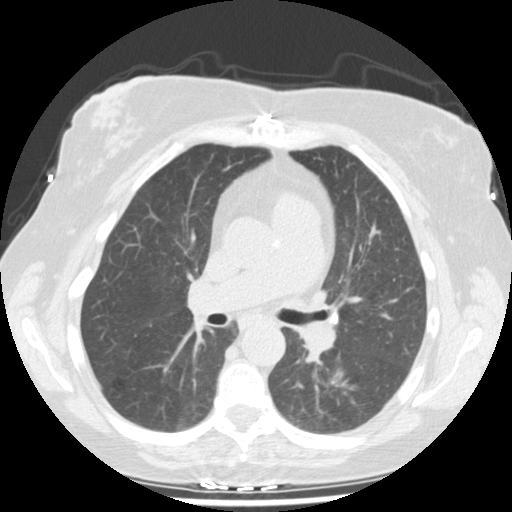
Chest CT (low-dose screening protocol), one axial image; second screening round (one year after baseline); lung window (W 1500 / L -600 HU); standard (soft-tissue) reconstruction kernel (STANDARD); 120 kVp; 512 × 512 image matrix. Female, age 61 years at enrolment. Current smoker at enrolment.
- Lesion marked by an expert reader, bounding box <311,355,370,408> (left, top, right, bottom; pixels).
- The screening reader recorded 2 non-calcified nodules or masses ≥4 mm on this exam; which of them this box marks is not recorded.
- Official screen result: positive, change unspecified: nodule(s) >= 4 mm or enlarging nodule(s), mass(es), or other non-specific abnormalities suspicious for lung cancer.